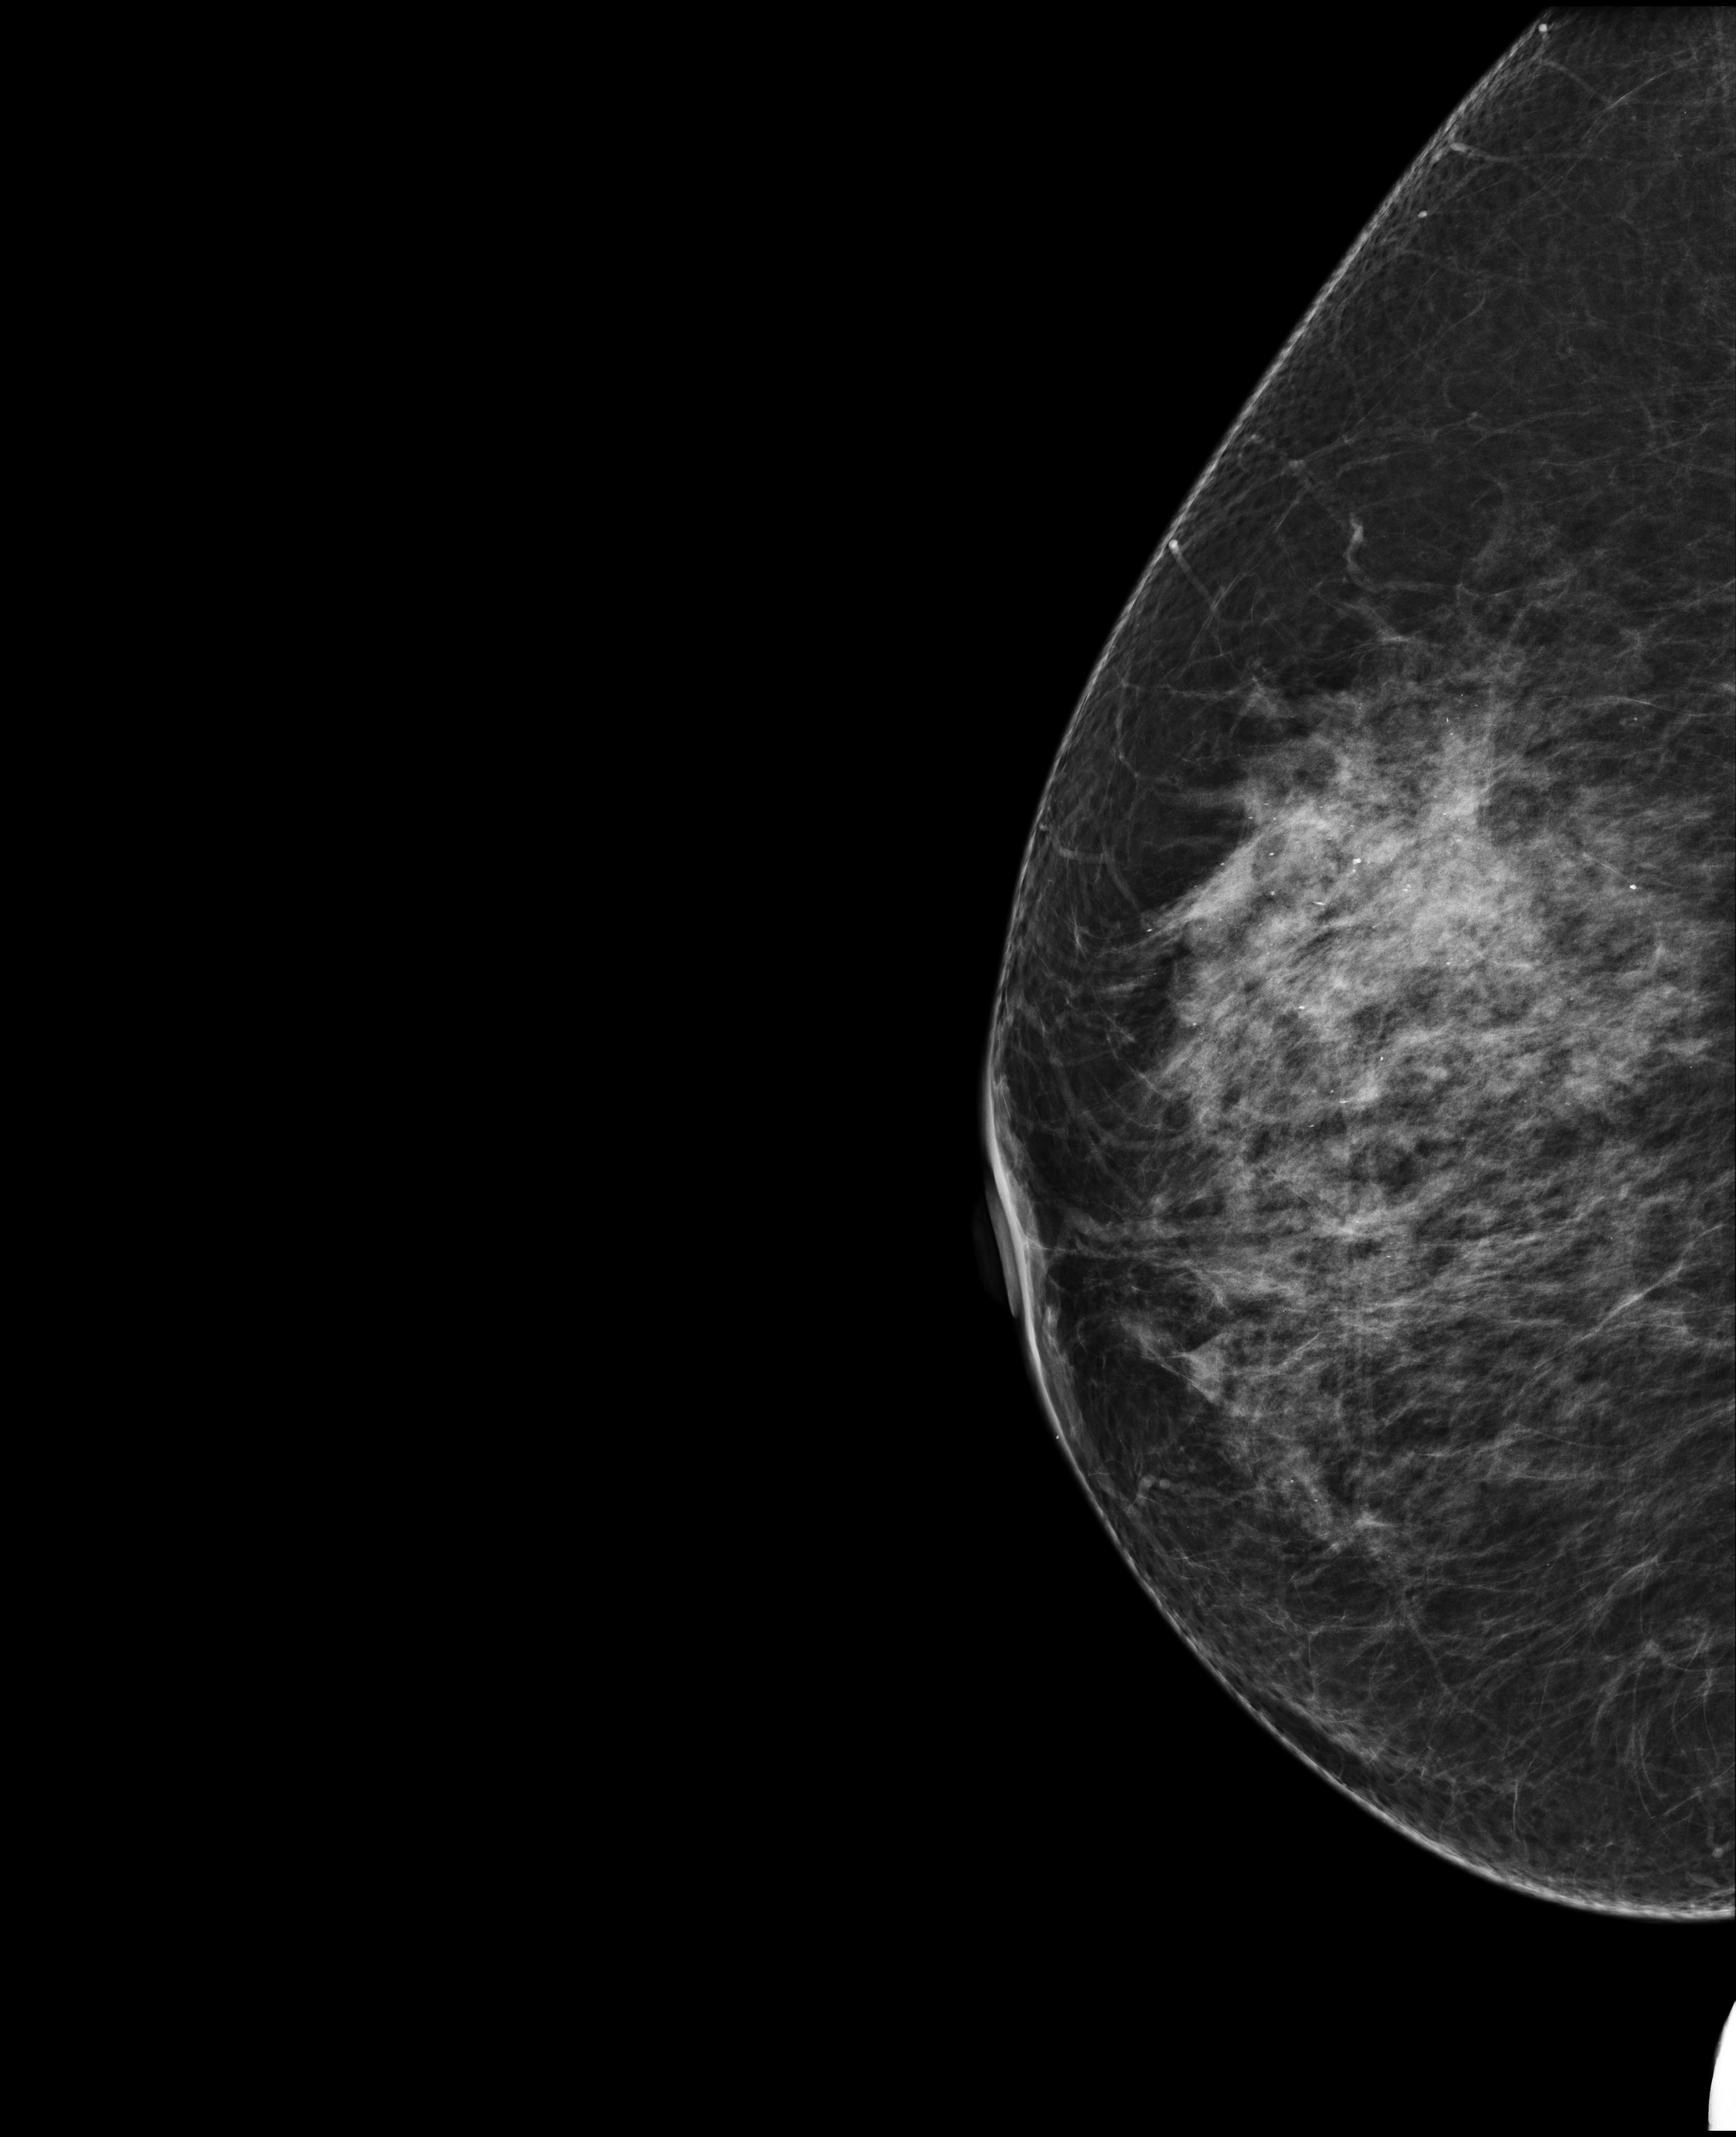
Diagnostic examination (additional views), compressed breast thickness 60 mm. Patient aged 71 years (female).
Image type: full-field digital mammogram. Breast: right. Projection: ML view. BI-RADS breast density category at the screening exam (both breasts, scale 1–4): 3. Final BI-RADS assessment for this screening round (tomosynthesis exam, both breasts): category 1. Recall: recalled for additional imaging after this screen.